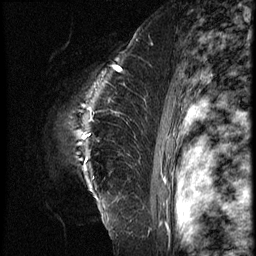
Breast MRI (dynamic contrast-enhanced), one sagittal slice. 3 images stored at this slice position (order not interpretable as contrast timing). 1.5 T. TE 4.2 ms, TR 9 ms. 2.5 mm slice thickness. 256 × 256 image matrix, field of view 180 × 180 mm. Patient: female, 39 years. From the clinical record (not read from this slice): setting: breast cancer imaged before/during neoadjuvant chemotherapy; receptor status: HER2-positive.
Annotated regions visible in this slice (semi-automatic segmentation, software-assisted and operator-edited):
- analysis volume of interest (the breast-tissue region the enhancement analysis was run in; not a lesion): box from (x=30, y=64) to (x=152, y=228) px
- tumour enhancement mask (voxels above the 140 % enhancement threshold inside the analysis volume of interest): (x=84, y=66)–(x=123, y=138)